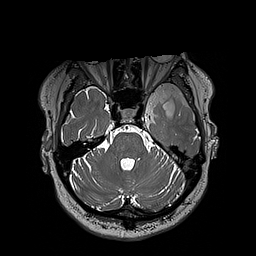
Brain MRI from a brain-tumour surgery series, one axial slice; 1 mm slice thickness; 256 × 256 image matrix, field of view 250 × 250 mm. Case-level facts recorded for this patient, not image findings: histopathology: Oligodendroglioma; WHO grade: 3; IDH mutation: yes; tumour location: Left Sylvian Fissure (Temporal).
Structures marked on this image (manually delineated by an expert):
- tumour: bounding box [x1, y1, x2, y2] px = [153, 83, 194, 116]